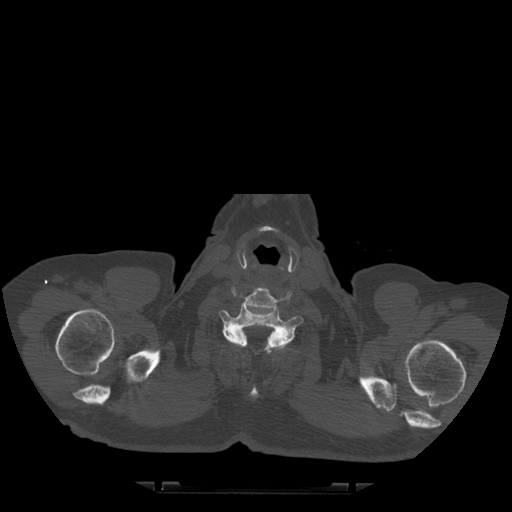
CT including the spine, one axial slice. Slice 452 of 522 in the series (ordered by position). Bone window (W 1800 / L 400 HU). 512 × 512 image matrix. Patient age 72 years. From the clinical record (not read from this slice): primary cancer: prostate.
Annotated regions visible in this slice (semi-automatic segmentation, software-assisted and operator-edited):
- T1 vertebra: bounding box (x1, y1, x2, y2) in pixels: (223, 331, 283, 397)